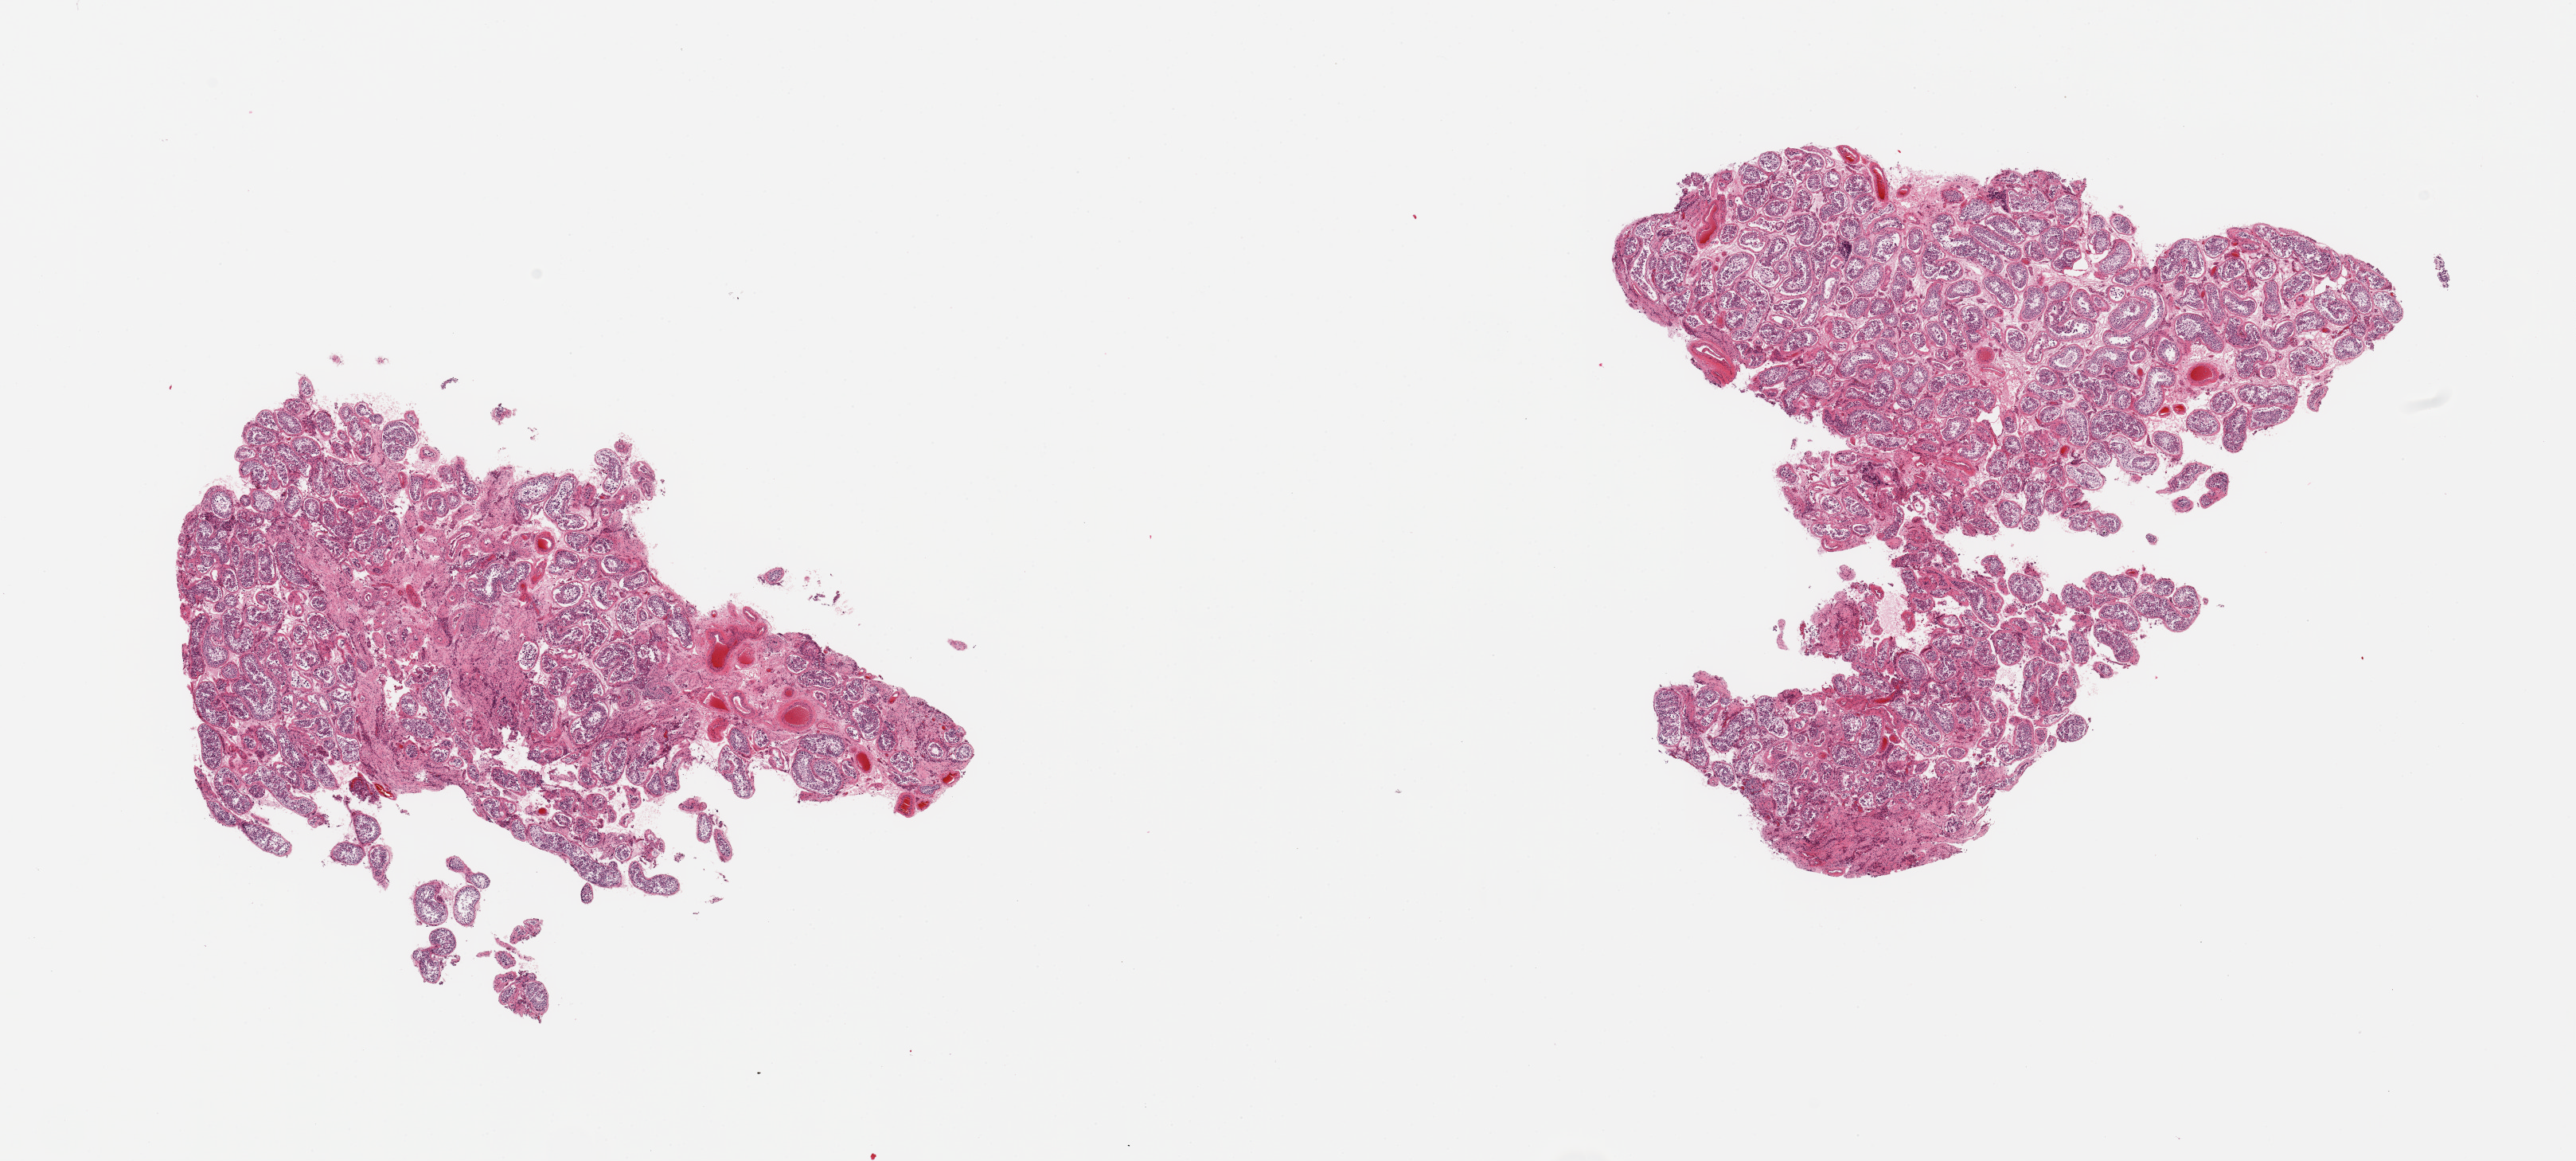
Digitized haematoxylin and eosin-stained section, low-resolution overview of the scanned area, about 25.6 x 11.5 mm (acquisition: 20x scan). PAXgene-fixed paraffin-embedded (PFPE) section. Section of testis (target tissue). Donor tissue sample. Donor: male.
Review note (as recorded): 2 pieces, focal infarcts; Leydig cells well seen.